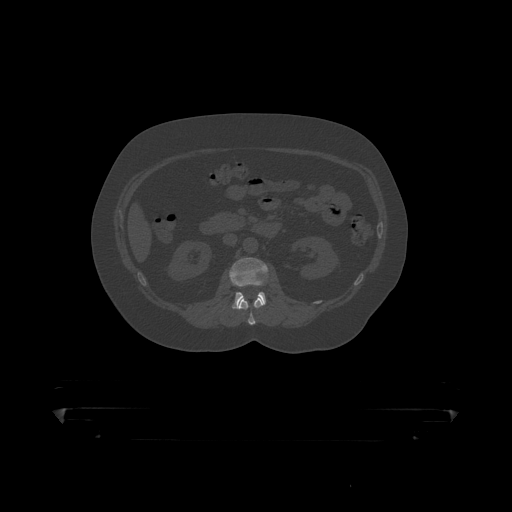
CT including the spine, one axial slice; slice 130 of 390 in the series (ordered by position); reconstruction kernel STANDARD; 120 kVp; bone window (W 1800 / L 400 HU); 1.25 mm slice thickness; 512 × 512 image matrix, field of view 650 × 650 mm. Patient: male, 60 years. Case-level facts recorded for this patient, not image findings: primary cancer: prostate.
Outlined on this slice (semi-automatic segmentation, software-assisted and operator-edited):
- L1 vertebra: box from (x=239, y=299) to (x=264, y=319) px
- L2 vertebra: (x=230, y=258)–(x=268, y=310)